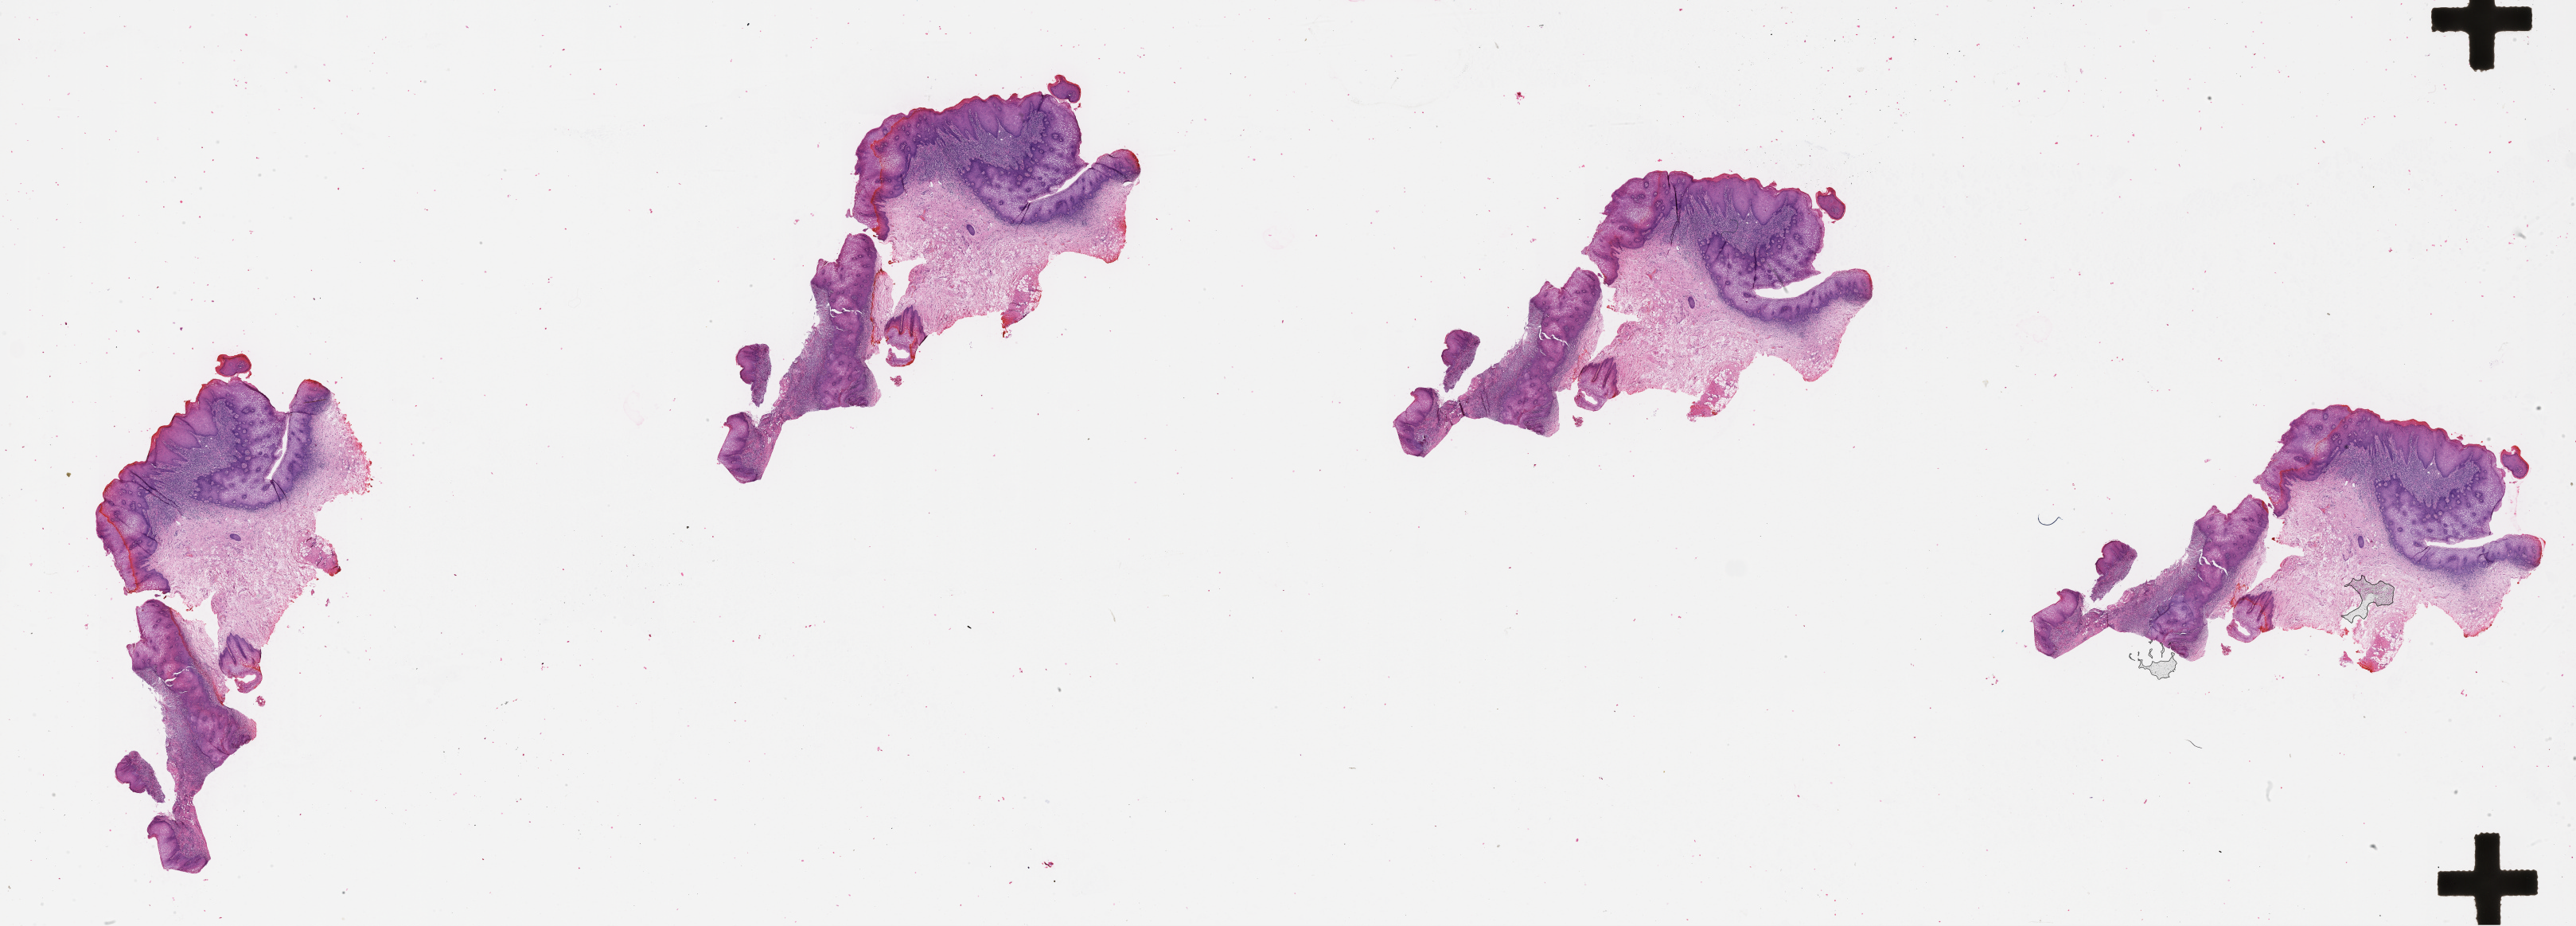
H&E-stained whole-slide image — a low-resolution overview of the entire scanned area, about 52.1 x 18.7 mm (slide scanned at 20x); normal (non-tumour) tissue sample, sampled site: buccal mucosa. Male, 69 y/o.
This section: normal (non-tumour) tissue from the same patient. Patient diagnosis: Squamous cell carcinoma, NOS (cheek mucosa).